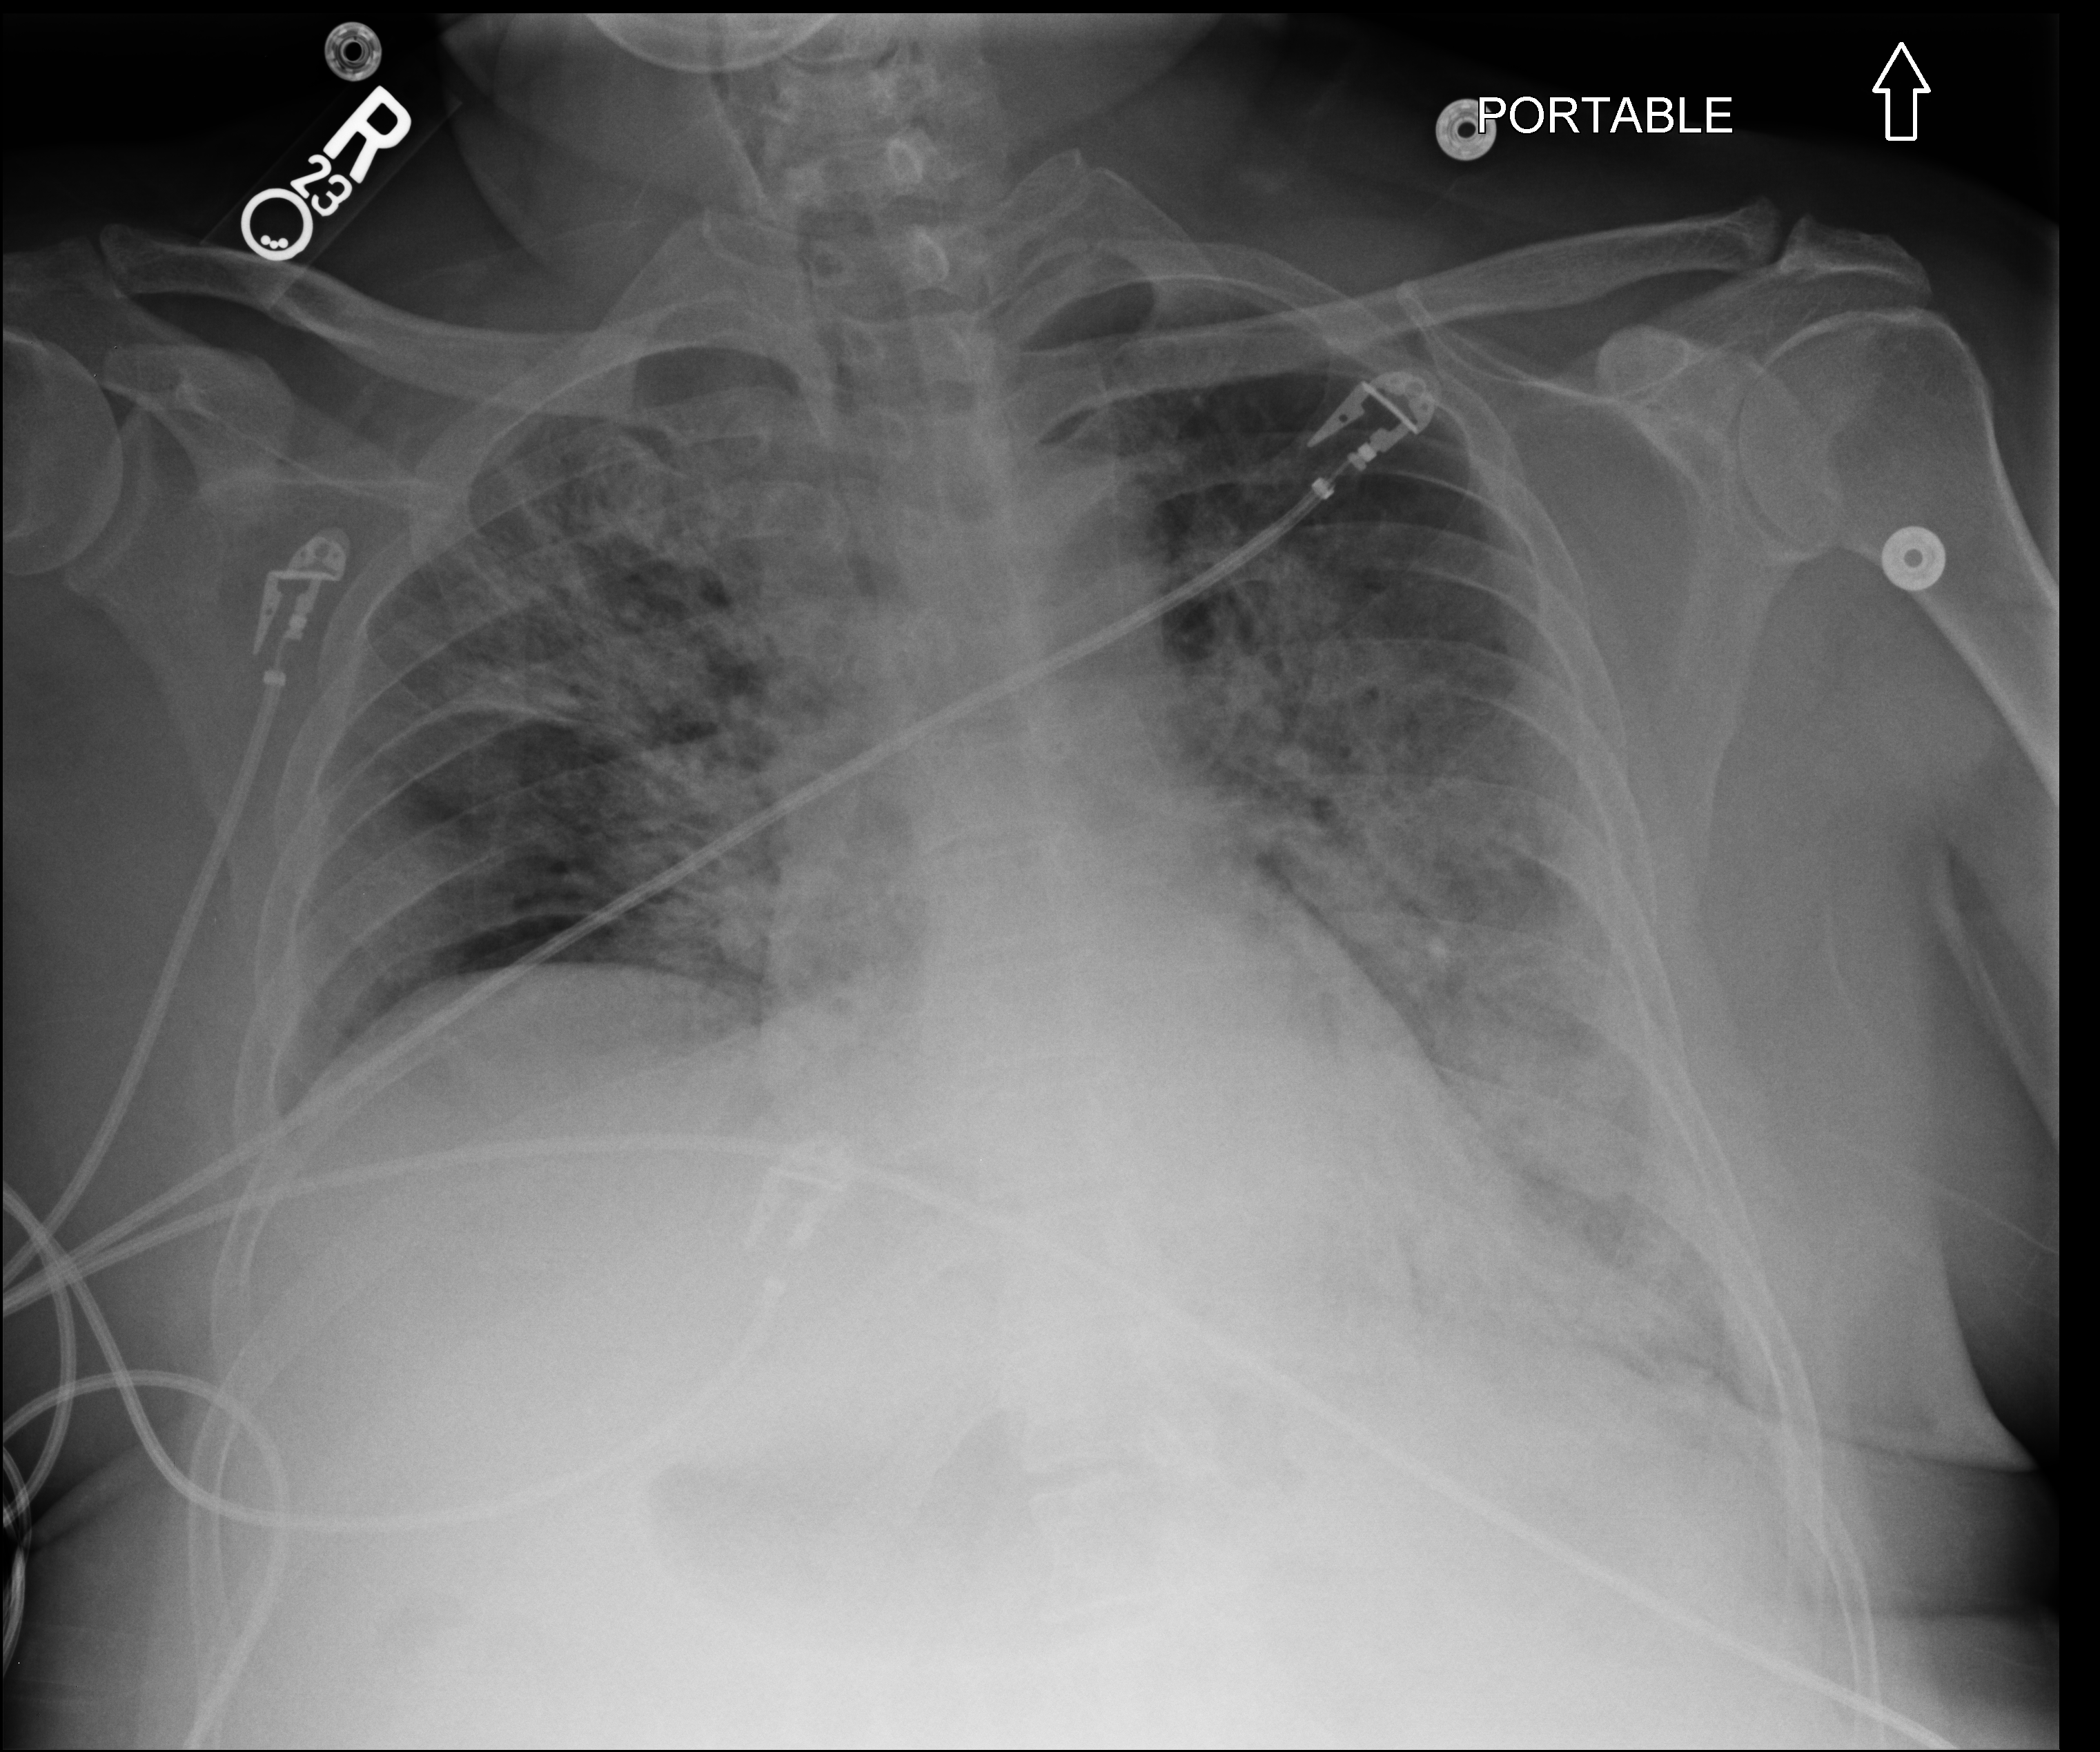
Chest X-ray (portable). Patient hospitalised with COVID-19; male, aged 18–59 years.
From the hospital-stay record, not from the radiograph (when in the stay this image was taken is not recorded): COPD (admission record): no; mechanically ventilated during this hospital stay: yes.